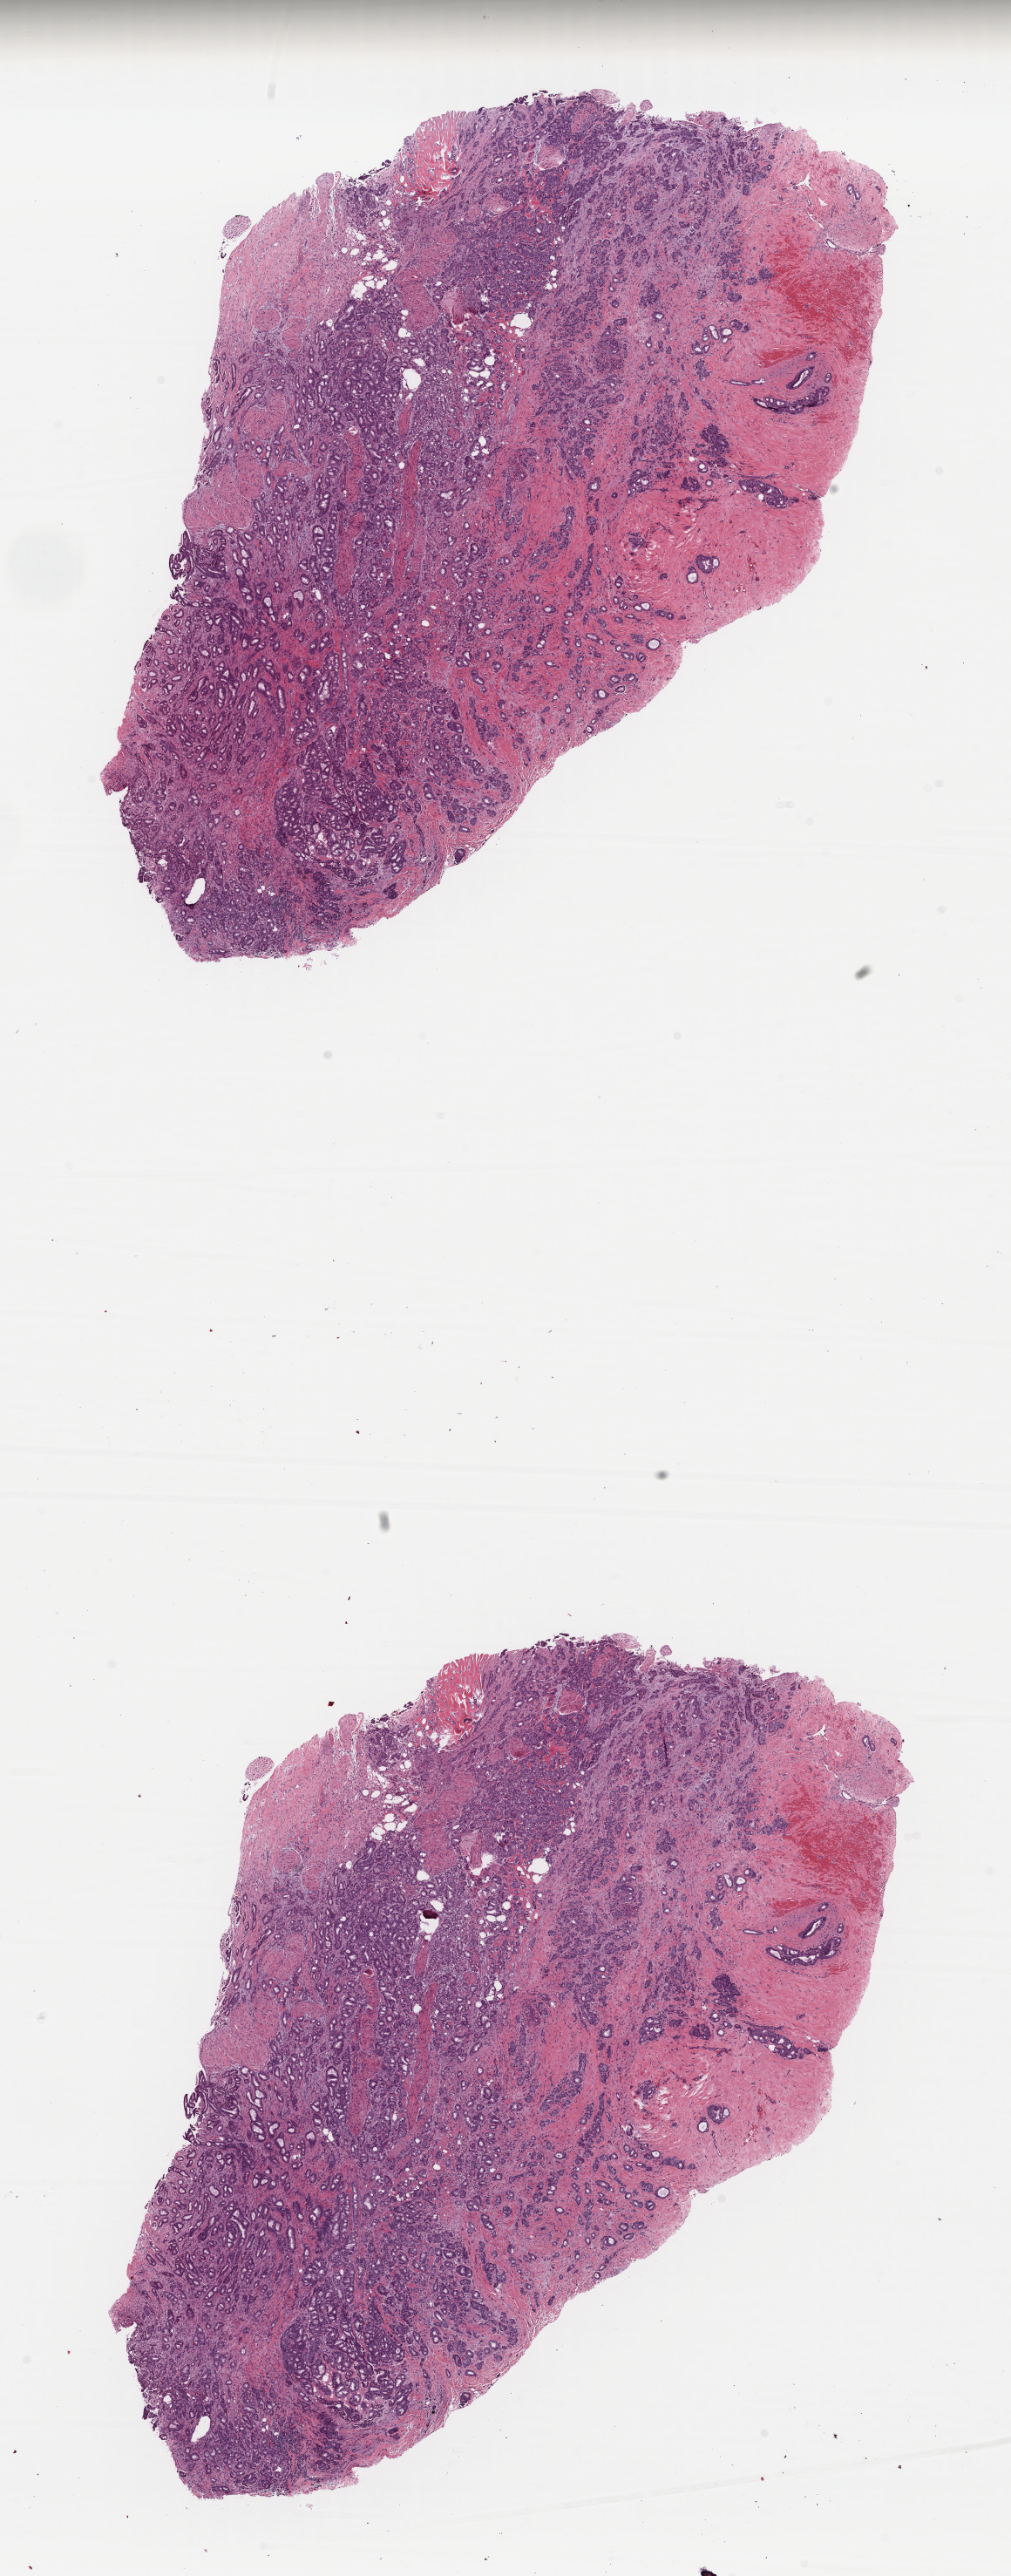
Whole-slide histology image, H&E-stained, a low-resolution overview of the entire scanned area, about 9.2 x 23.3 mm (acquisition: 40x scan). Formalin-fixed paraffin-embedded (FFPE) diagnostic section. Primary tumour sample from the breast. Patient: female, age at initial diagnosis 79 years.
TNM: T2 N0 (i-) M0. AJCC pathologic stage: IIA. Diagnosis: Infiltrating duct carcinoma, NOS.